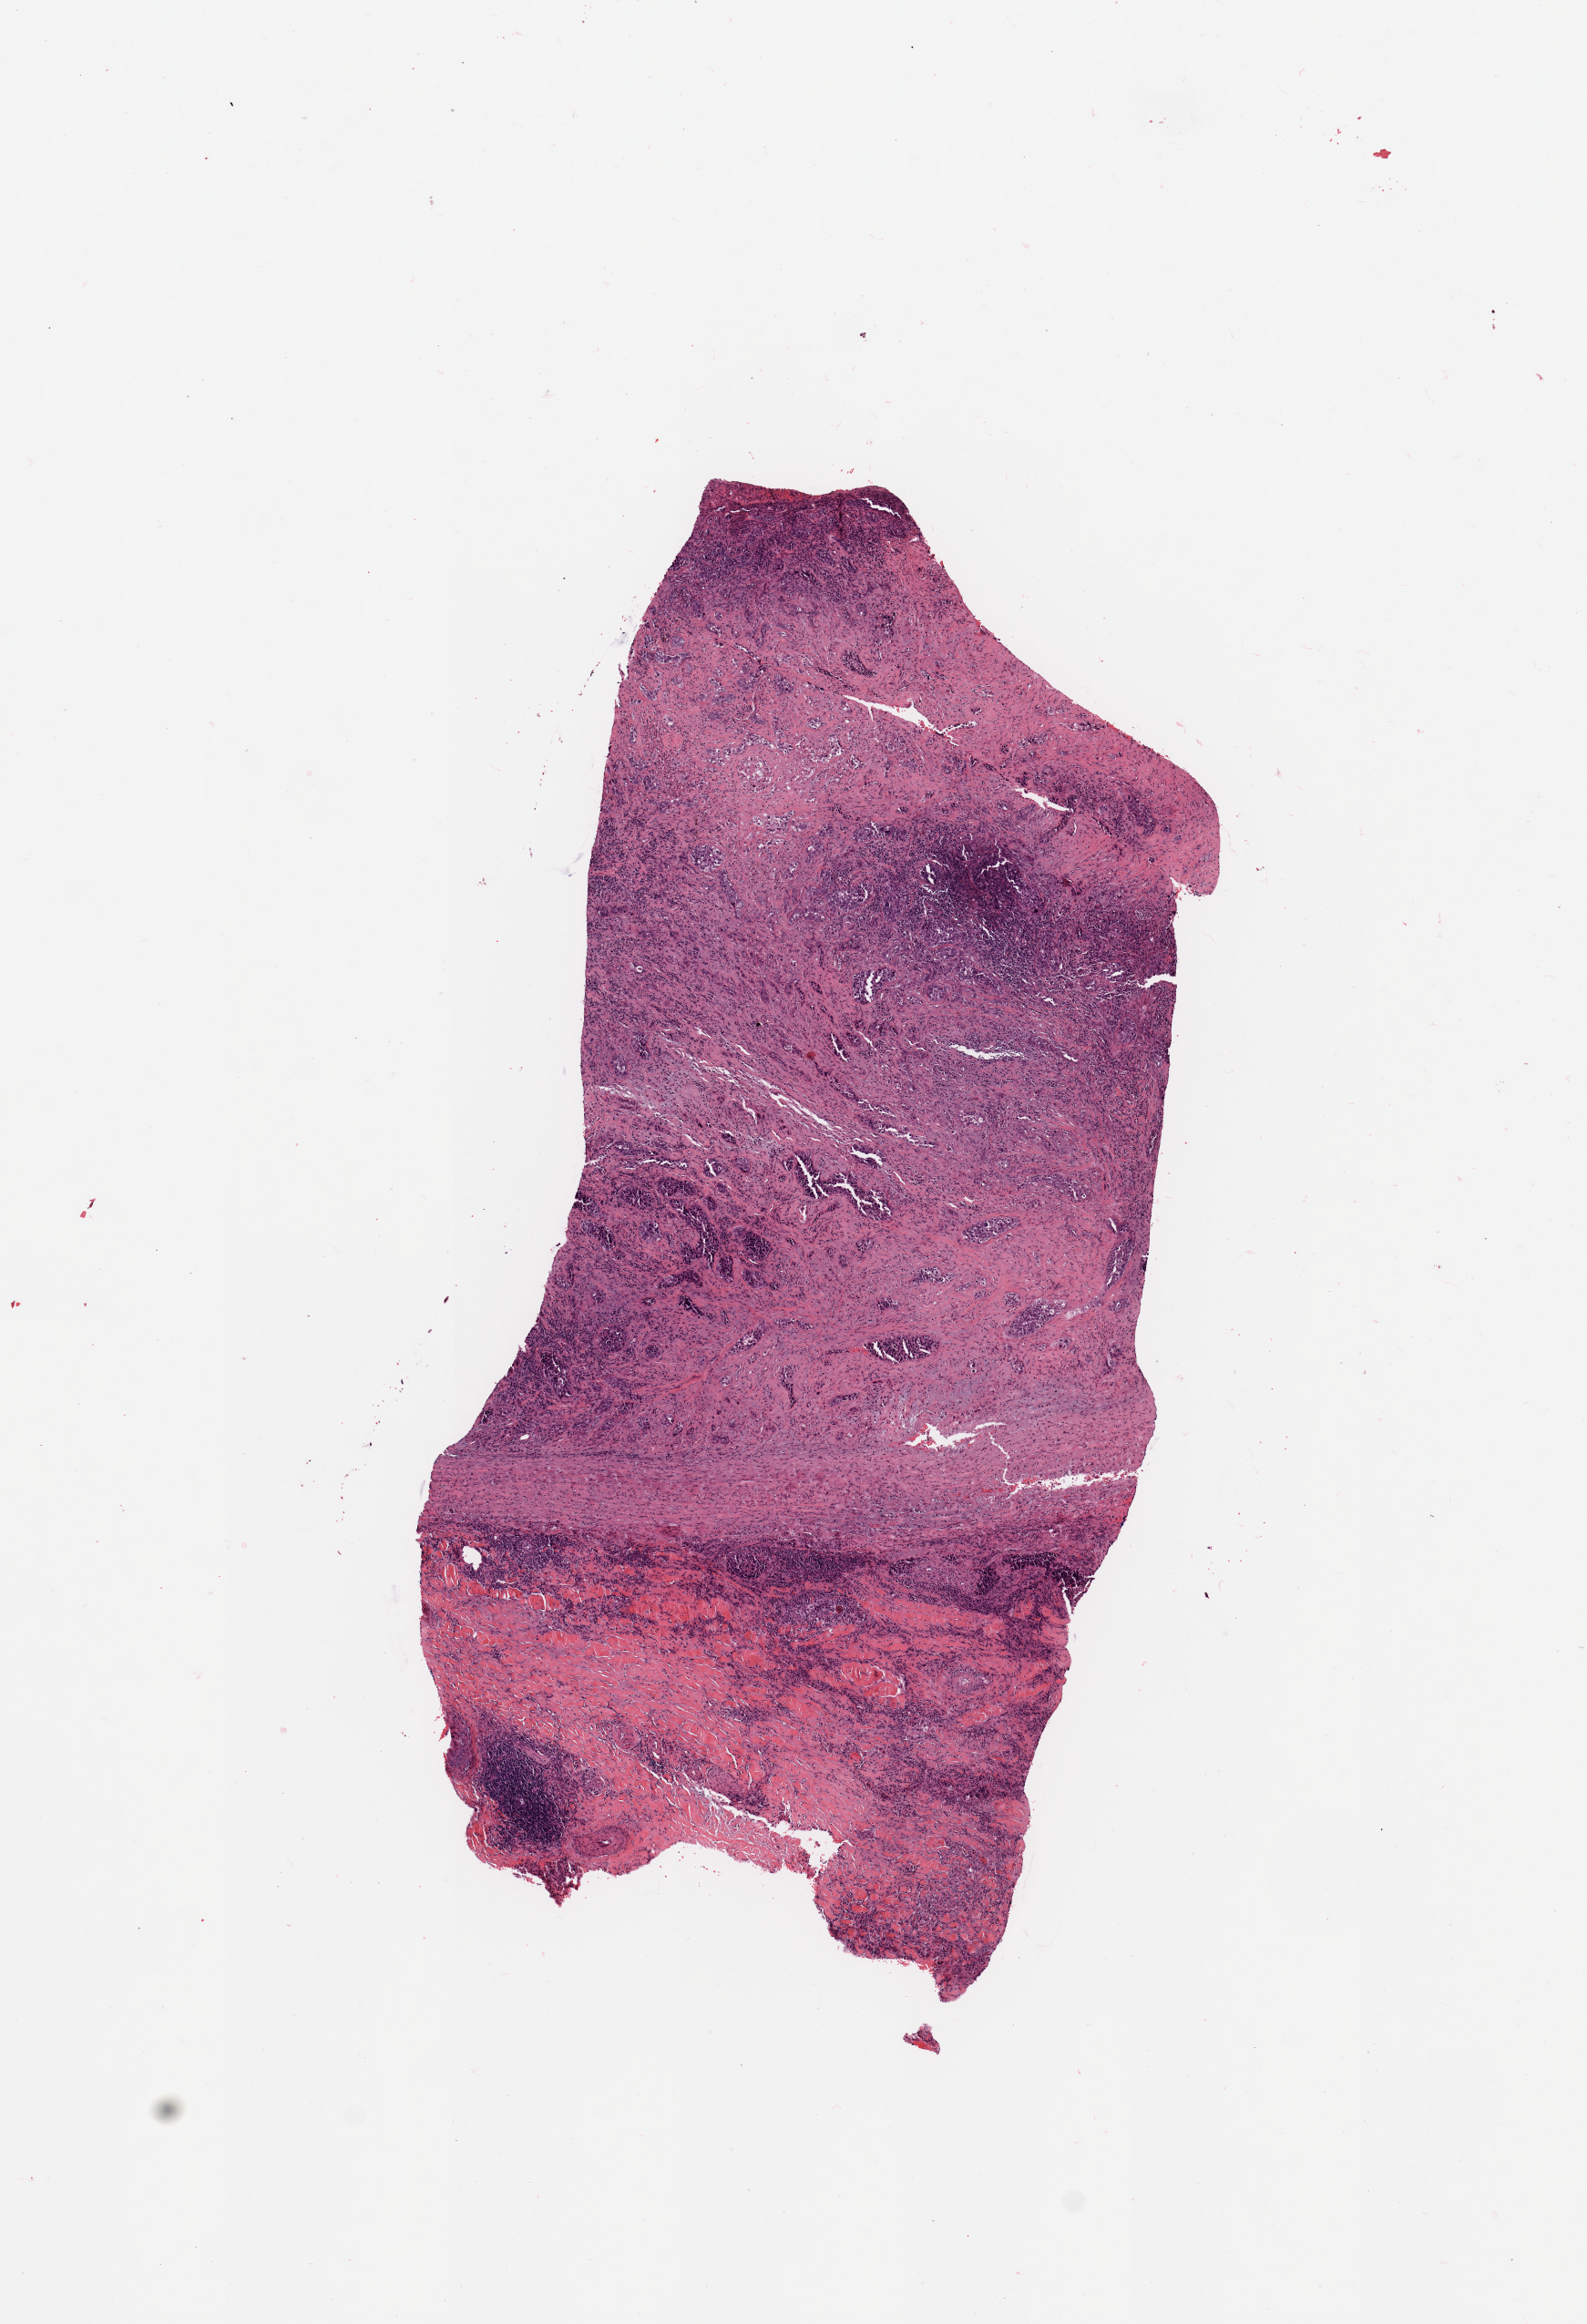
Hematoxylin and eosin (H&E) stained whole-slide image — shown as a low-resolution overview of the whole scanned area (about 6.9 x 10.1 mm), tumour tissue sample, lung. Male, 88 y/o. Histologic grade: G3 (poorly differentiated).
AJCC pathologic stage: IIA. Primary tumour site (as recorded): left lower lobe. Histologic diagnosis: Squamous cell carcinoma, NOS.